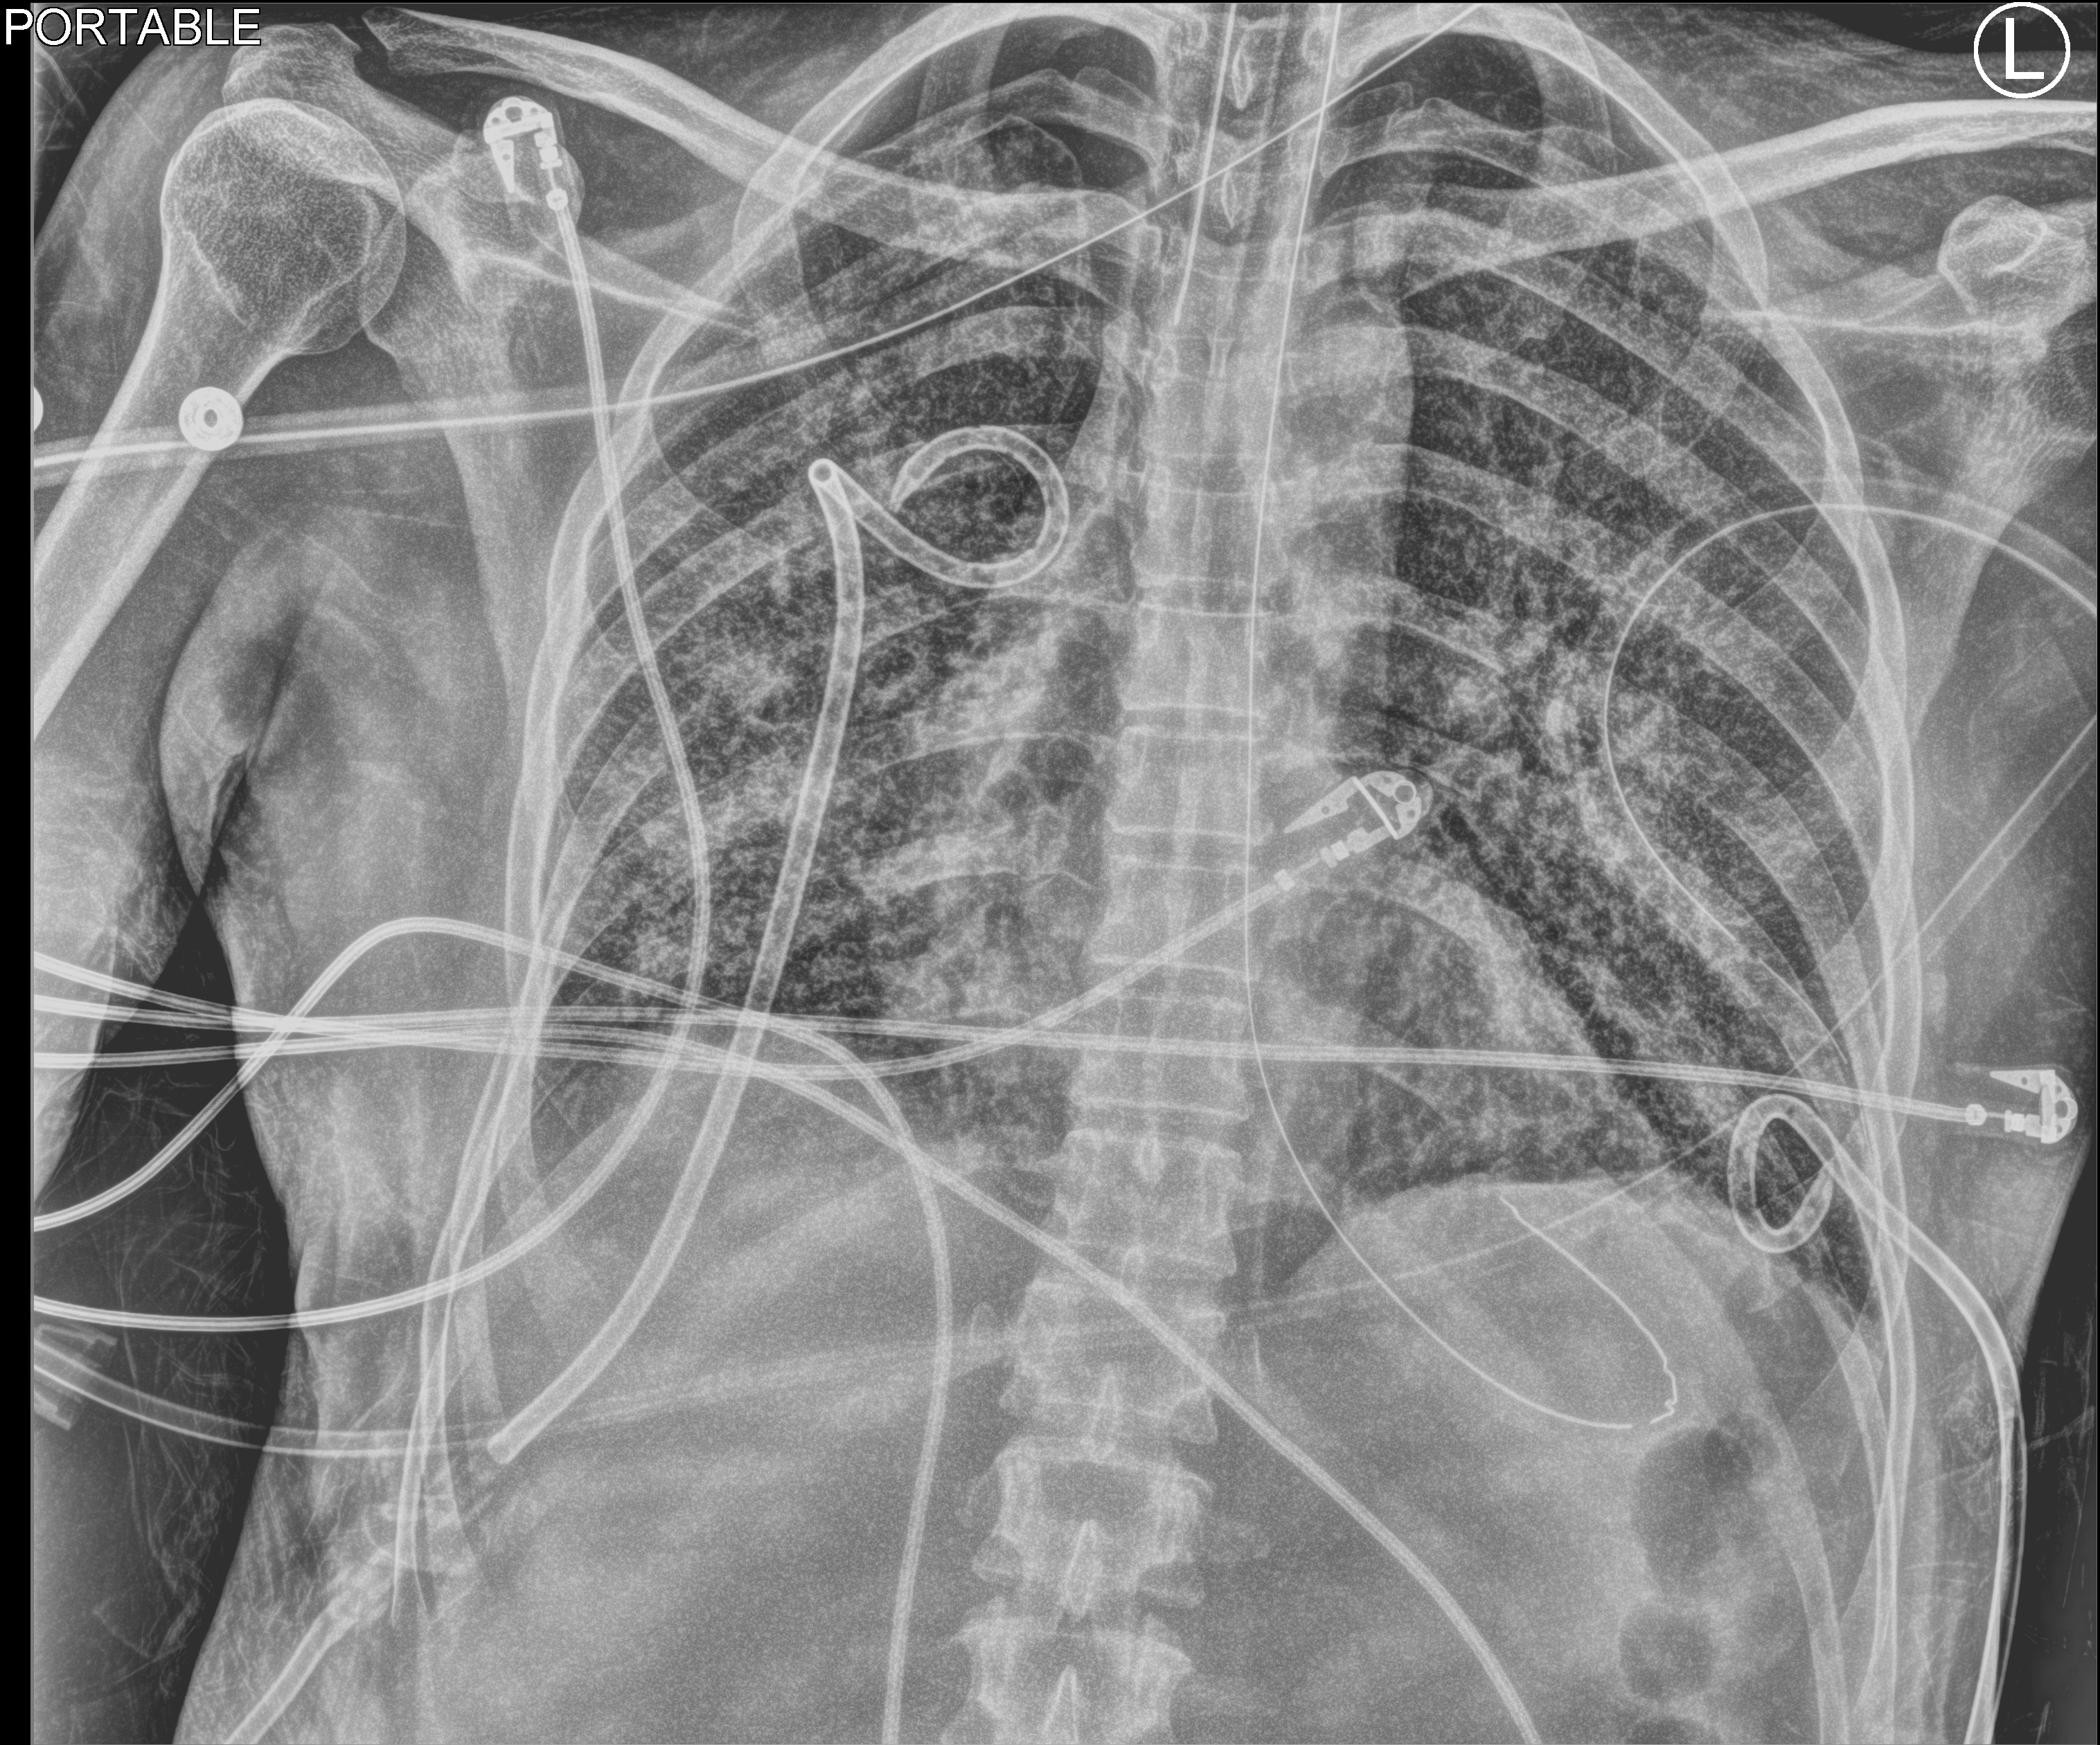
Bedside chest radiograph (computed radiography), anteroposterior (AP) projection. Patient hospitalised with COVID-19, aged 18–59 years.
From the hospital-stay record, not from the radiograph (when in the stay this image was taken is not recorded): other chronic lung disease (admission record): no; admitted to intensive care during this hospital stay: yes.